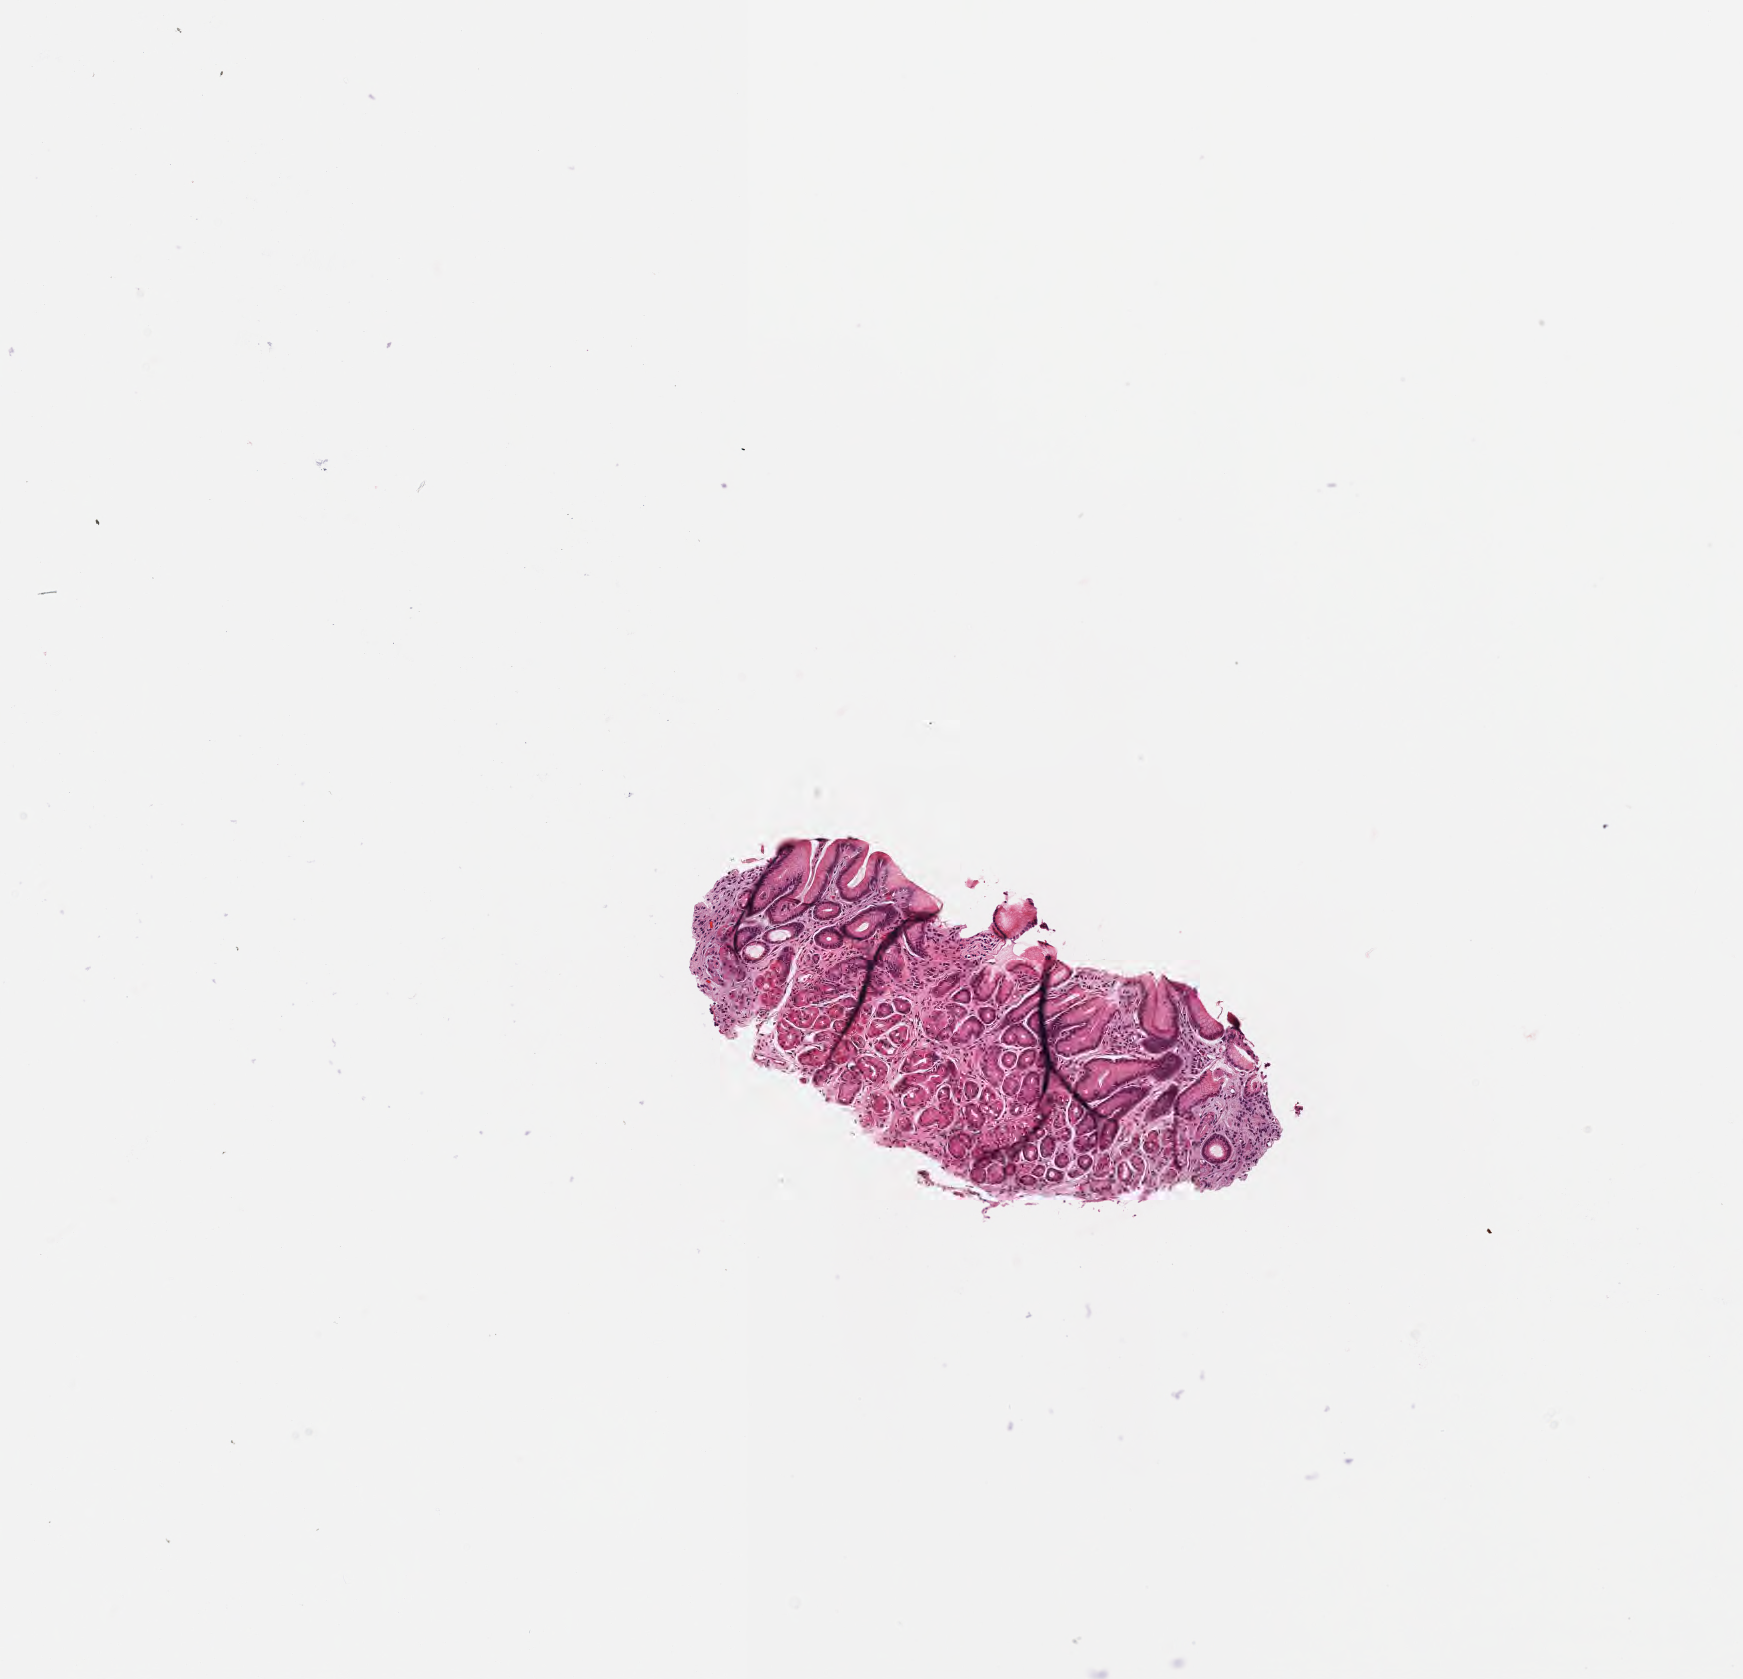
Whole-slide image, haematoxylin and eosin stain, low-resolution overview of the scanned area, about 3.5 x 3.4 mm. Formalin-fixed, paraffin-embedded (FFPE) tissue. Specimen: non-tumor (normal tissue) sample from a patient with burkitt lymphoma, NOS. Female patient, 74 years old. Composition of this section per pathologist review: tumor cells 0%, tumor nuclei 0%.
This section: non-tumor tissue sample; the patient's diagnosis is given above. Section: bottom of the tissue portion.